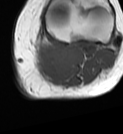
MRI of an extremity soft-tissue mass, one axial slice. MR volume resampled by the dataset authors to the PET/CT grid (not the native acquisition matrix). 3.27 mm slice thickness. 123 × 134 image matrix. Female patient. Case-level facts recorded for this patient, not image findings: histological type: extraskeletal high grade osteogenic sarcoma; grade: high; site of the primary tumour: left calf.
Outlined on this slice (expert contour drawn on MRI and transferred to this co-registered scan by the dataset authors):
- gross tumour volume (mass): box from (x=33, y=41) to (x=80, y=78) px